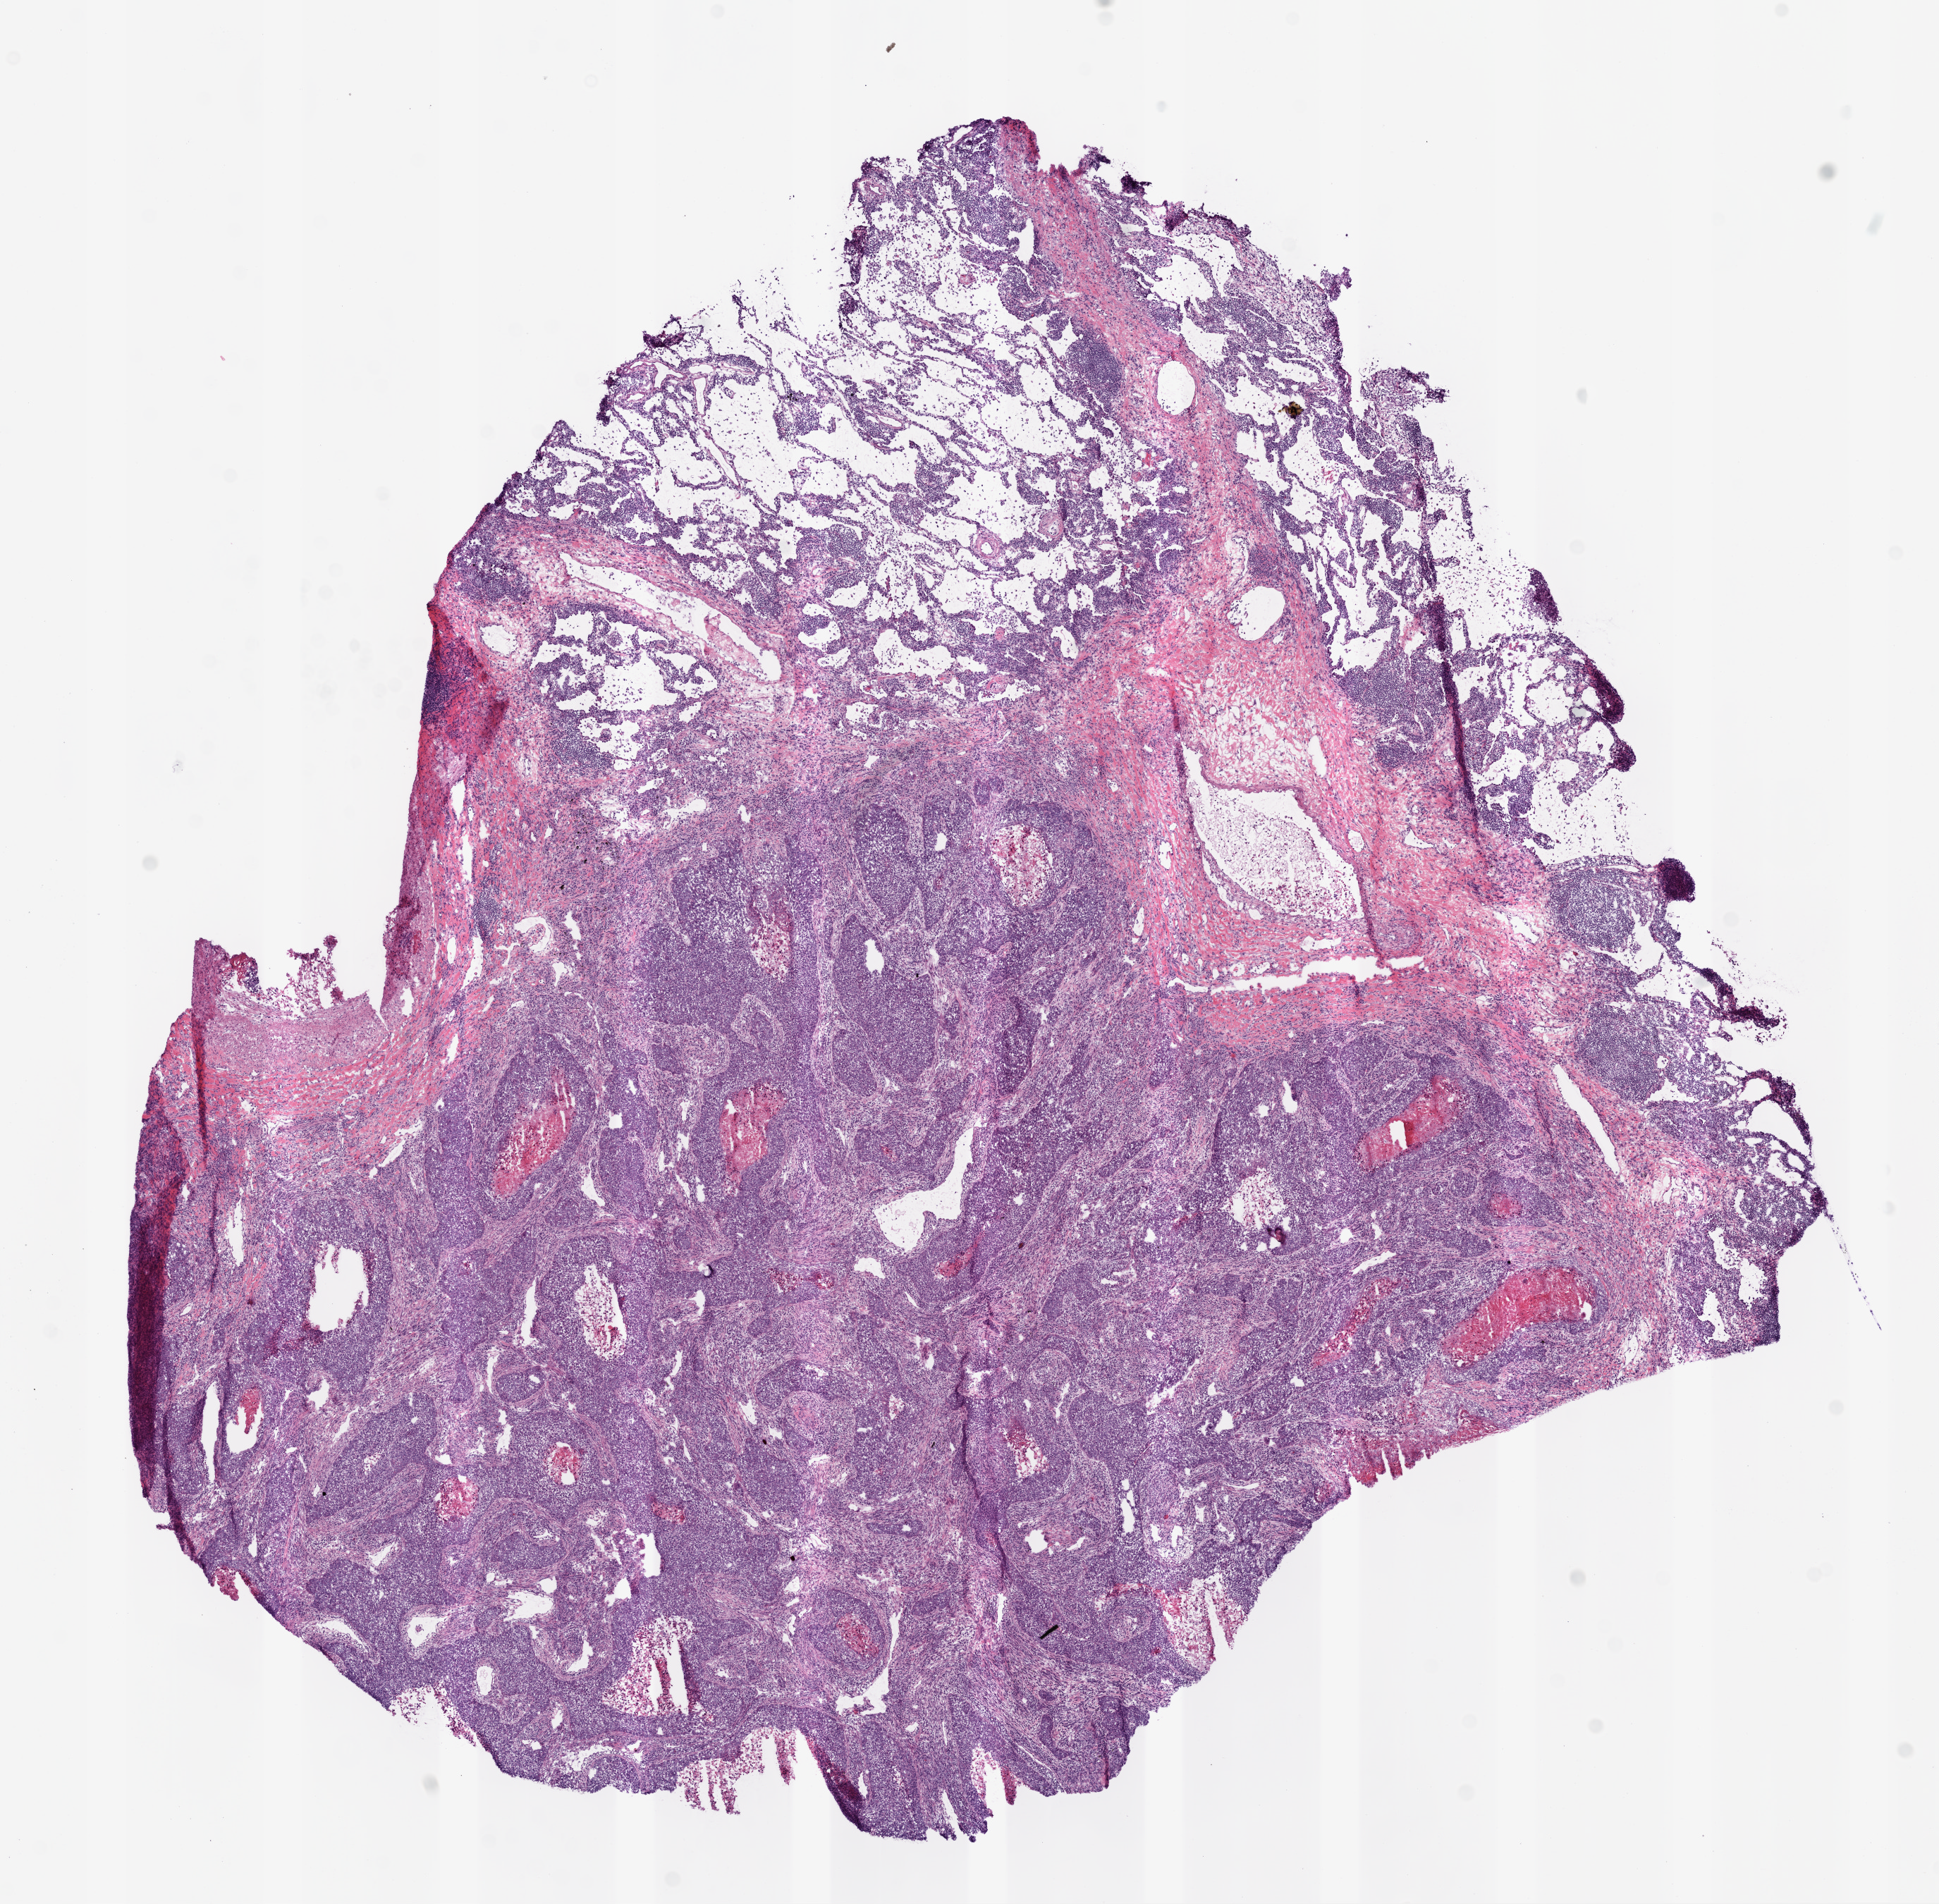
H&E whole-slide image — whole scanned area (about 11.0 x 10.8 mm, slide scanned at 20x) shown as a low-resolution overview. Frozen section. Lung, primary tumour sample. Patient: female, age at initial diagnosis 79 years. Pathologist review of this section (percent, as recorded): tumour cells 70%, tumour nuclei 85%, normal cells 15%, stromal cells 10%, necrosis 5%.
AJCC pathologic stage: IIB. Histologic diagnosis: Squamous cell carcinoma, NOS.